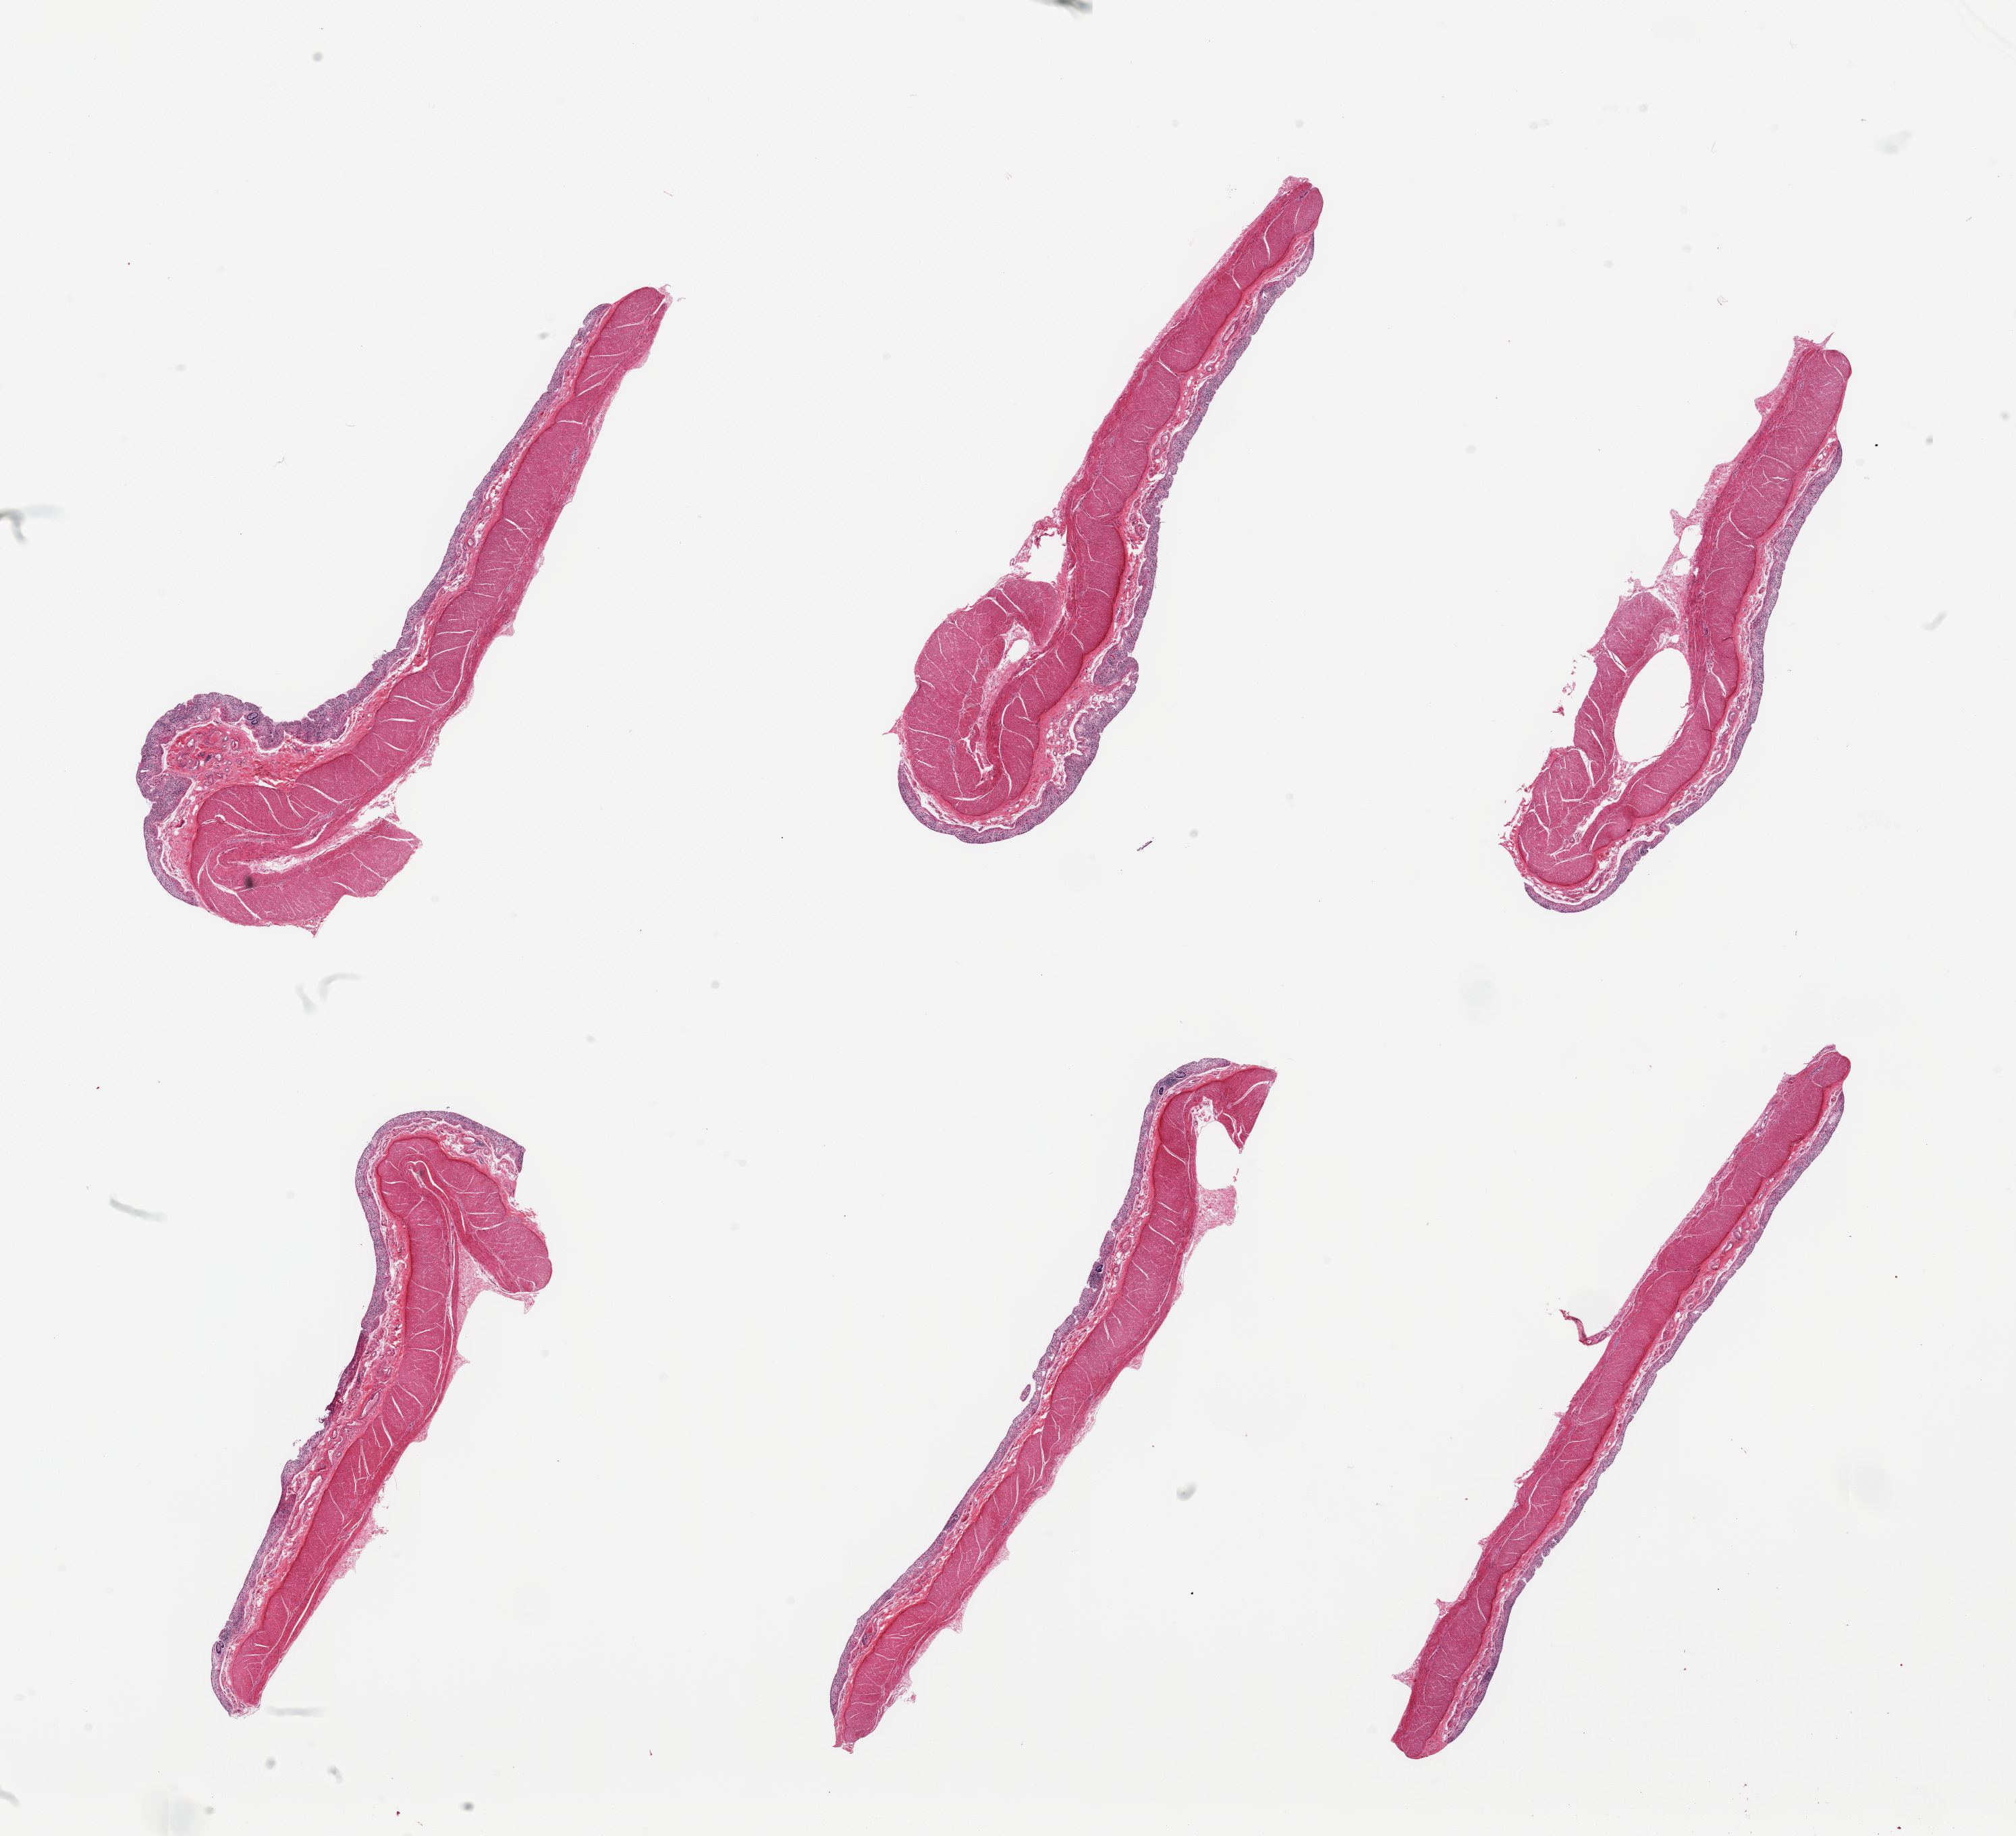
Digitized H&E-stained section — a low-resolution overview of the entire scanned area, about 23.6 x 21.5 mm, PAXgene-fixed paraffin-embedded (PFPE) section, sampled site (target tissue): transverse colon, tissue donor sample. Male donor.
Pathologist's review note for this sample: 6 pieces; full thickness sections, mucosa largely autolyzed.